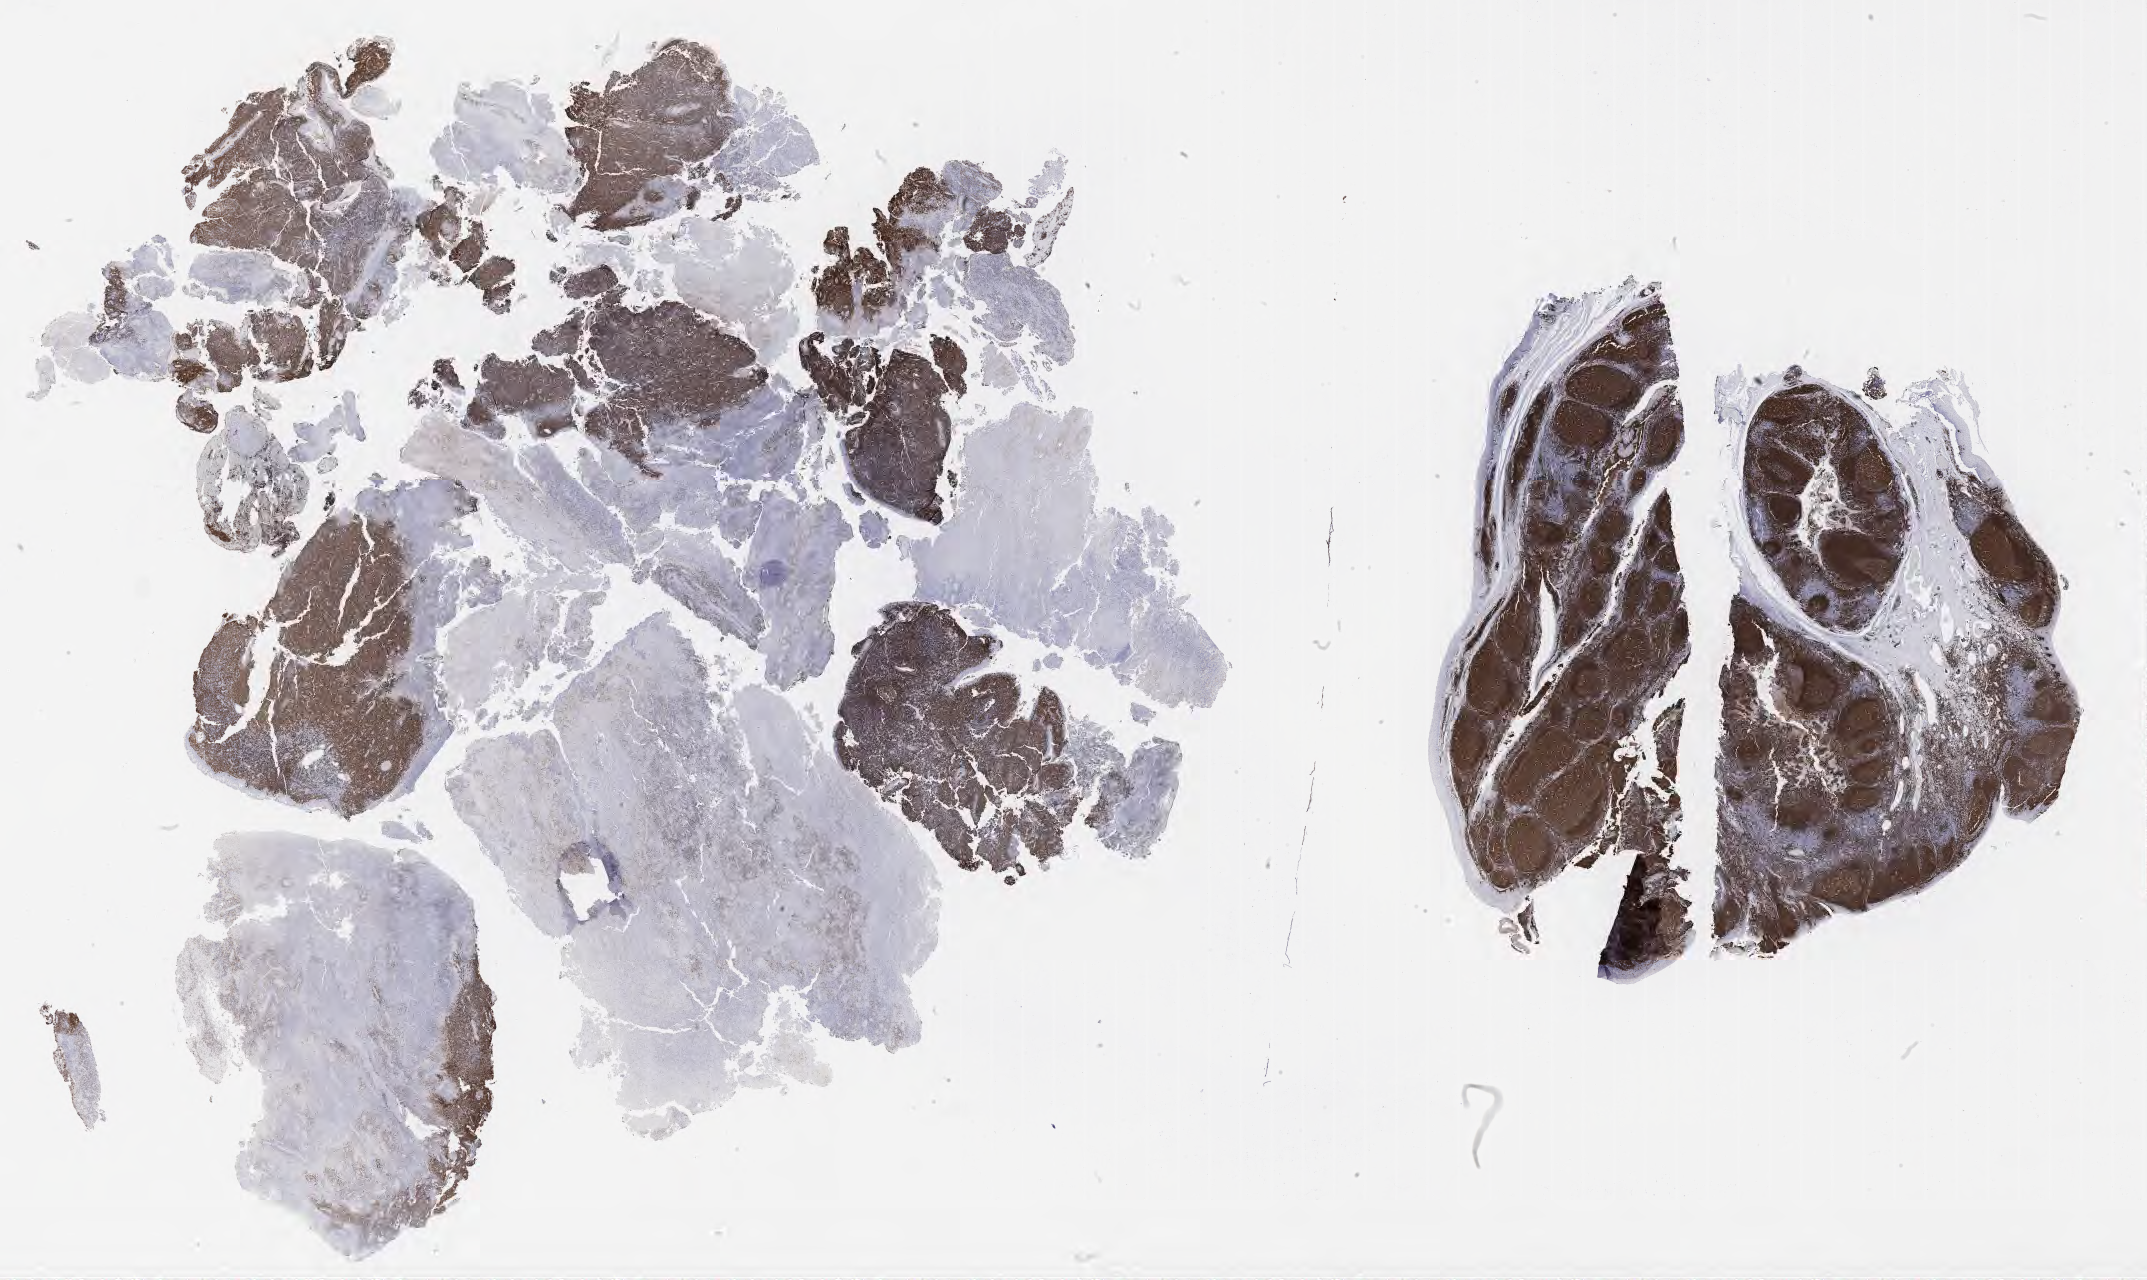
Whole-slide image, immunohistochemical stain for CD79a, low-resolution overview of the scanned area, about 34.7 x 20.7 mm; tumor tissue. Male patient, age 47 years.
Diagnosis: Diffuse large B-cell lymphoma, NOS.